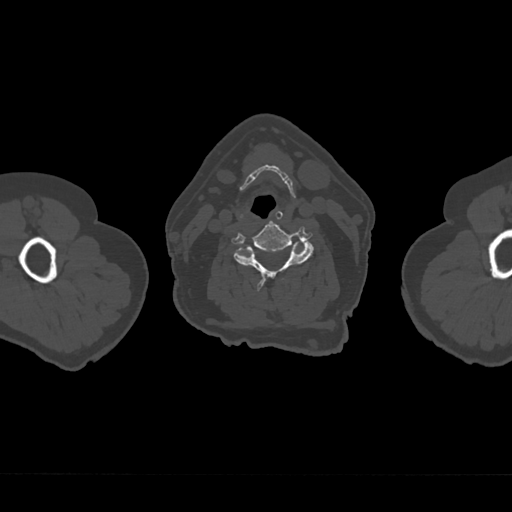
CT including the spine, one axial slice. Position 780 of 797 along the scan axis. Reconstruction kernel Br40s/3. 120 kVp. Bone window (W 1800 / L 400 HU). 0.5 mm slice thickness. 512 × 512 image matrix, field of view 377 × 377 mm. Male patient, age 75 years. Case-level facts recorded for this patient, not image findings: primary cancer: renal; vertebrae with lytic lesions (as recorded): T4.
Outlined on this slice (semi-automatic segmentation, software-assisted and operator-edited):
- T1 vertebra: box from (x=305, y=231) to (x=307, y=233) px